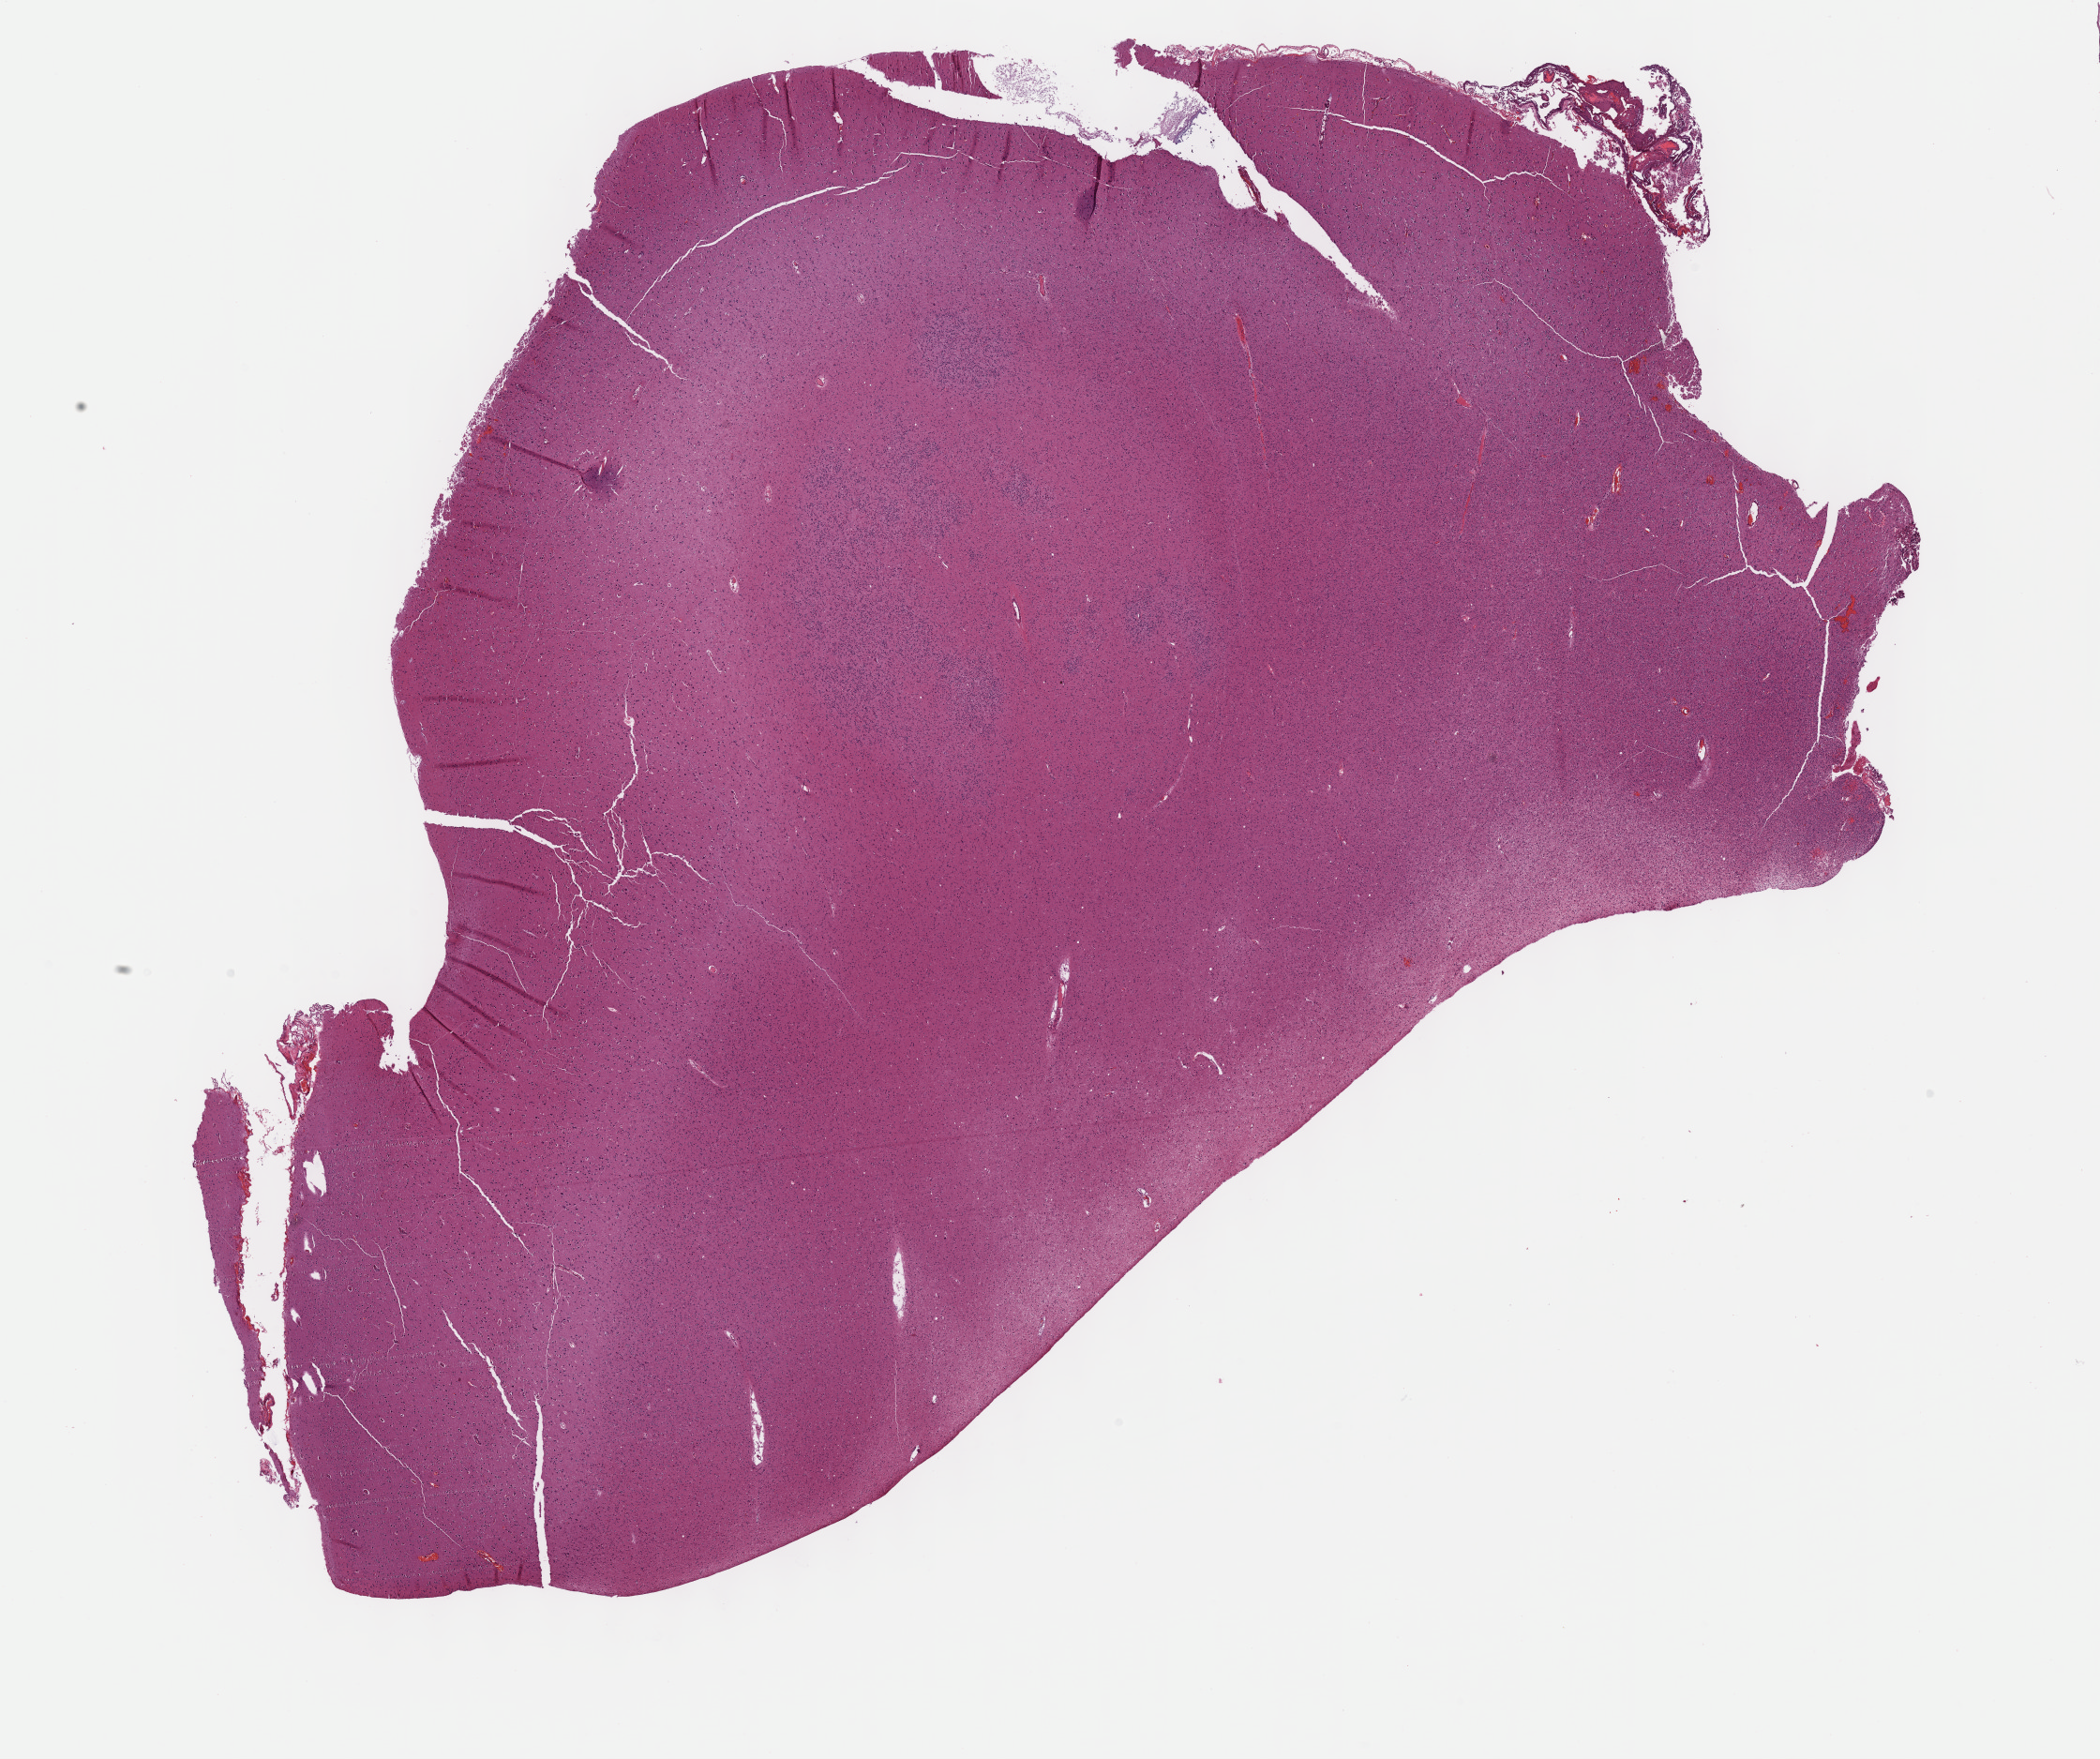
H&E-stained whole-slide image — shown as a low-resolution overview of the whole scanned area (about 18.1 x 15.2 mm, acquisition: 40x scan). Formalin-fixed paraffin-embedded (FFPE) diagnostic section. Brain, primary tumour sample. Male patient; age at initial diagnosis 40 years.
Diagnosis: Oligodendroglioma, anaplastic.